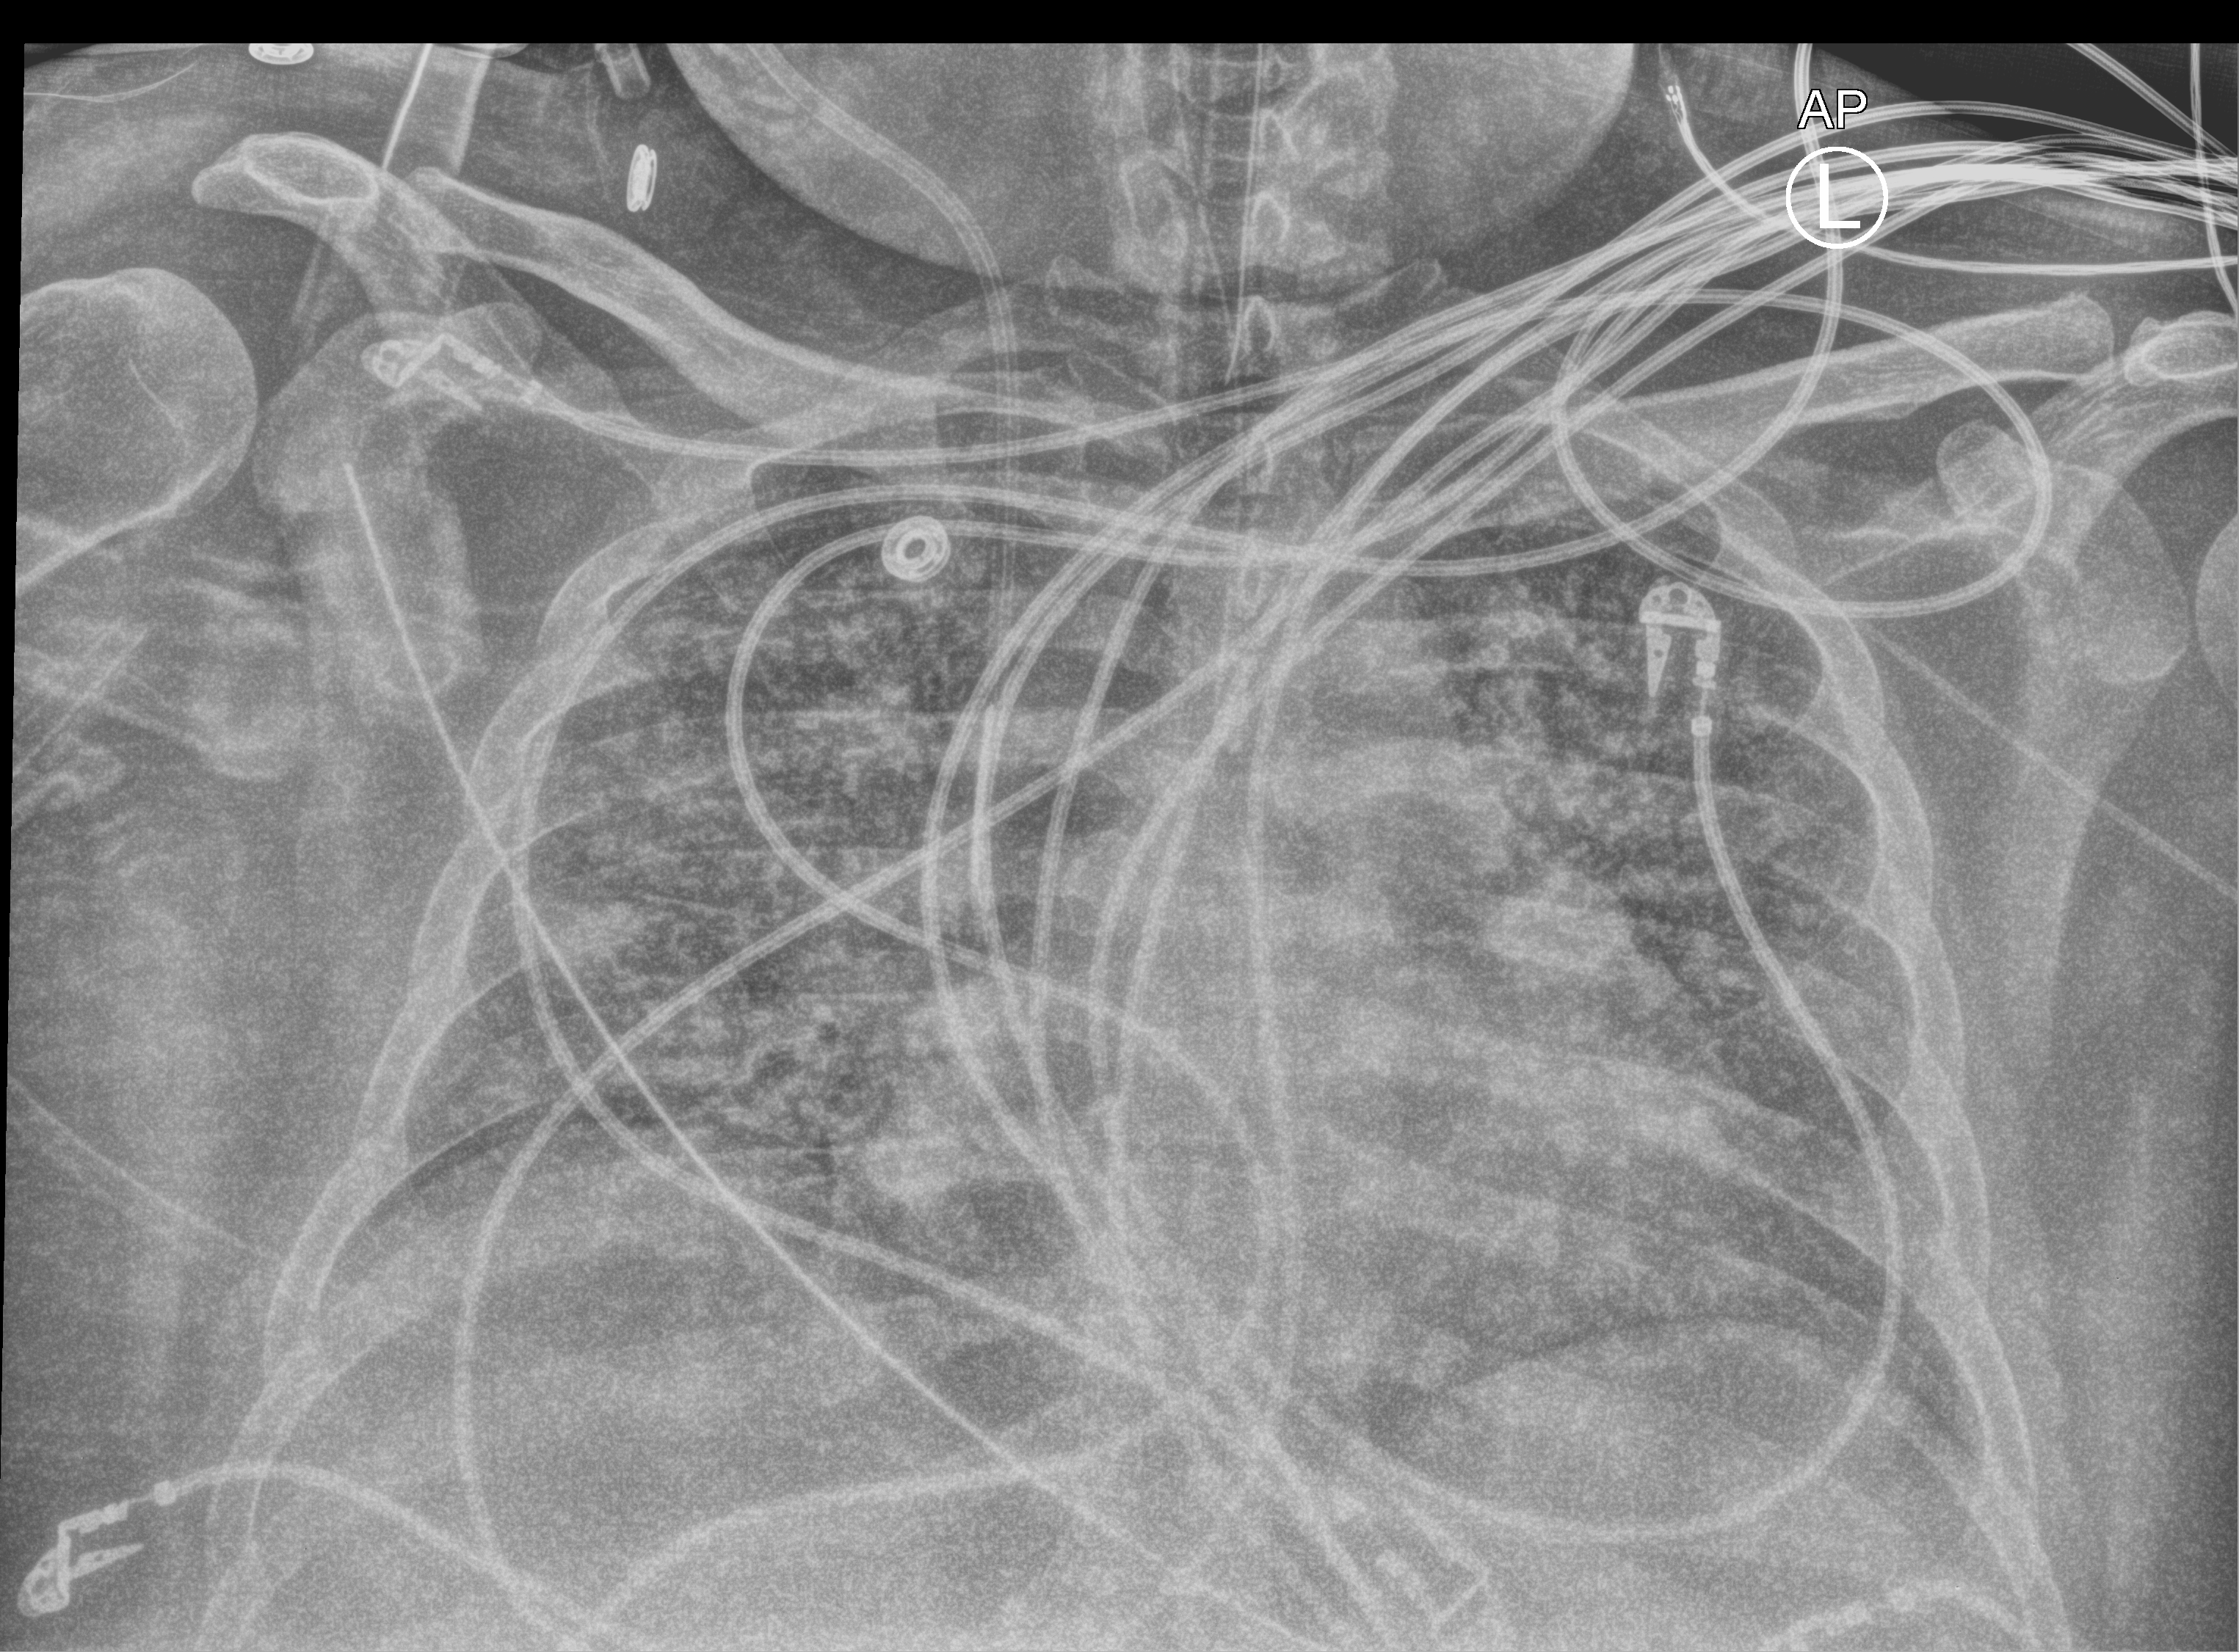
Chest X-ray (portable); anteroposterior (AP) projection. Patient hospitalised with COVID-19, aged 18–59 years.
Admission-level facts for this patient (not findings on this image; timing relative to this image not recorded):
- length of hospital stay: 22 days
- mechanically ventilated during this hospital stay: yes